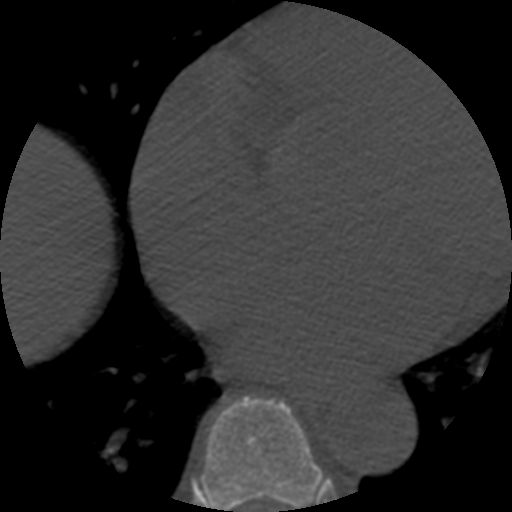
CT including the spine, one axial slice. Slice 326 of 508 in the series (ordered by position). 120 kVp. Bone window (W 1800 / L 400 HU). 1.25 mm slice thickness. 512 × 512 image matrix. Patient age 57 years. From the clinical record (not read from this slice): primary cancer: prostate.
Outlined on this slice (semi-automatic segmentation, software-assisted and operator-edited):
- T7 vertebra: bounding box [x1, y1, x2, y2] px = [200, 396, 325, 512]